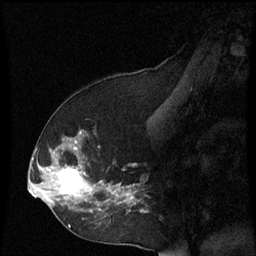
Breast MRI (dynamic contrast-enhanced), one sagittal slice; position 30 of 60 along the scan axis; dynamic contrast-enhanced series, image 2 of 3 at this slice position (ordered by acquisition); 1.5 T; TE 4.2 ms, TR 8.9 ms; 2 mm slice thickness; 256 × 256 image matrix, field of view 200 × 200 mm. Female patient, age 53 years. Case-level facts recorded for this patient, not image findings: setting: breast cancer imaged before/during neoadjuvant chemotherapy; receptor status: HR-positive, HER2-negative.
Annotated regions visible in this slice (semi-automatically segmented with operator editing):
- analysis volume of interest (the breast-tissue region the enhancement analysis was run in; not a lesion): bounding box <38,130,147,231> (left, top, right, bottom; pixels)
- tumour enhancement mask (voxels above the 70 % enhancement threshold inside the analysis volume of interest): <38,132,135,213>